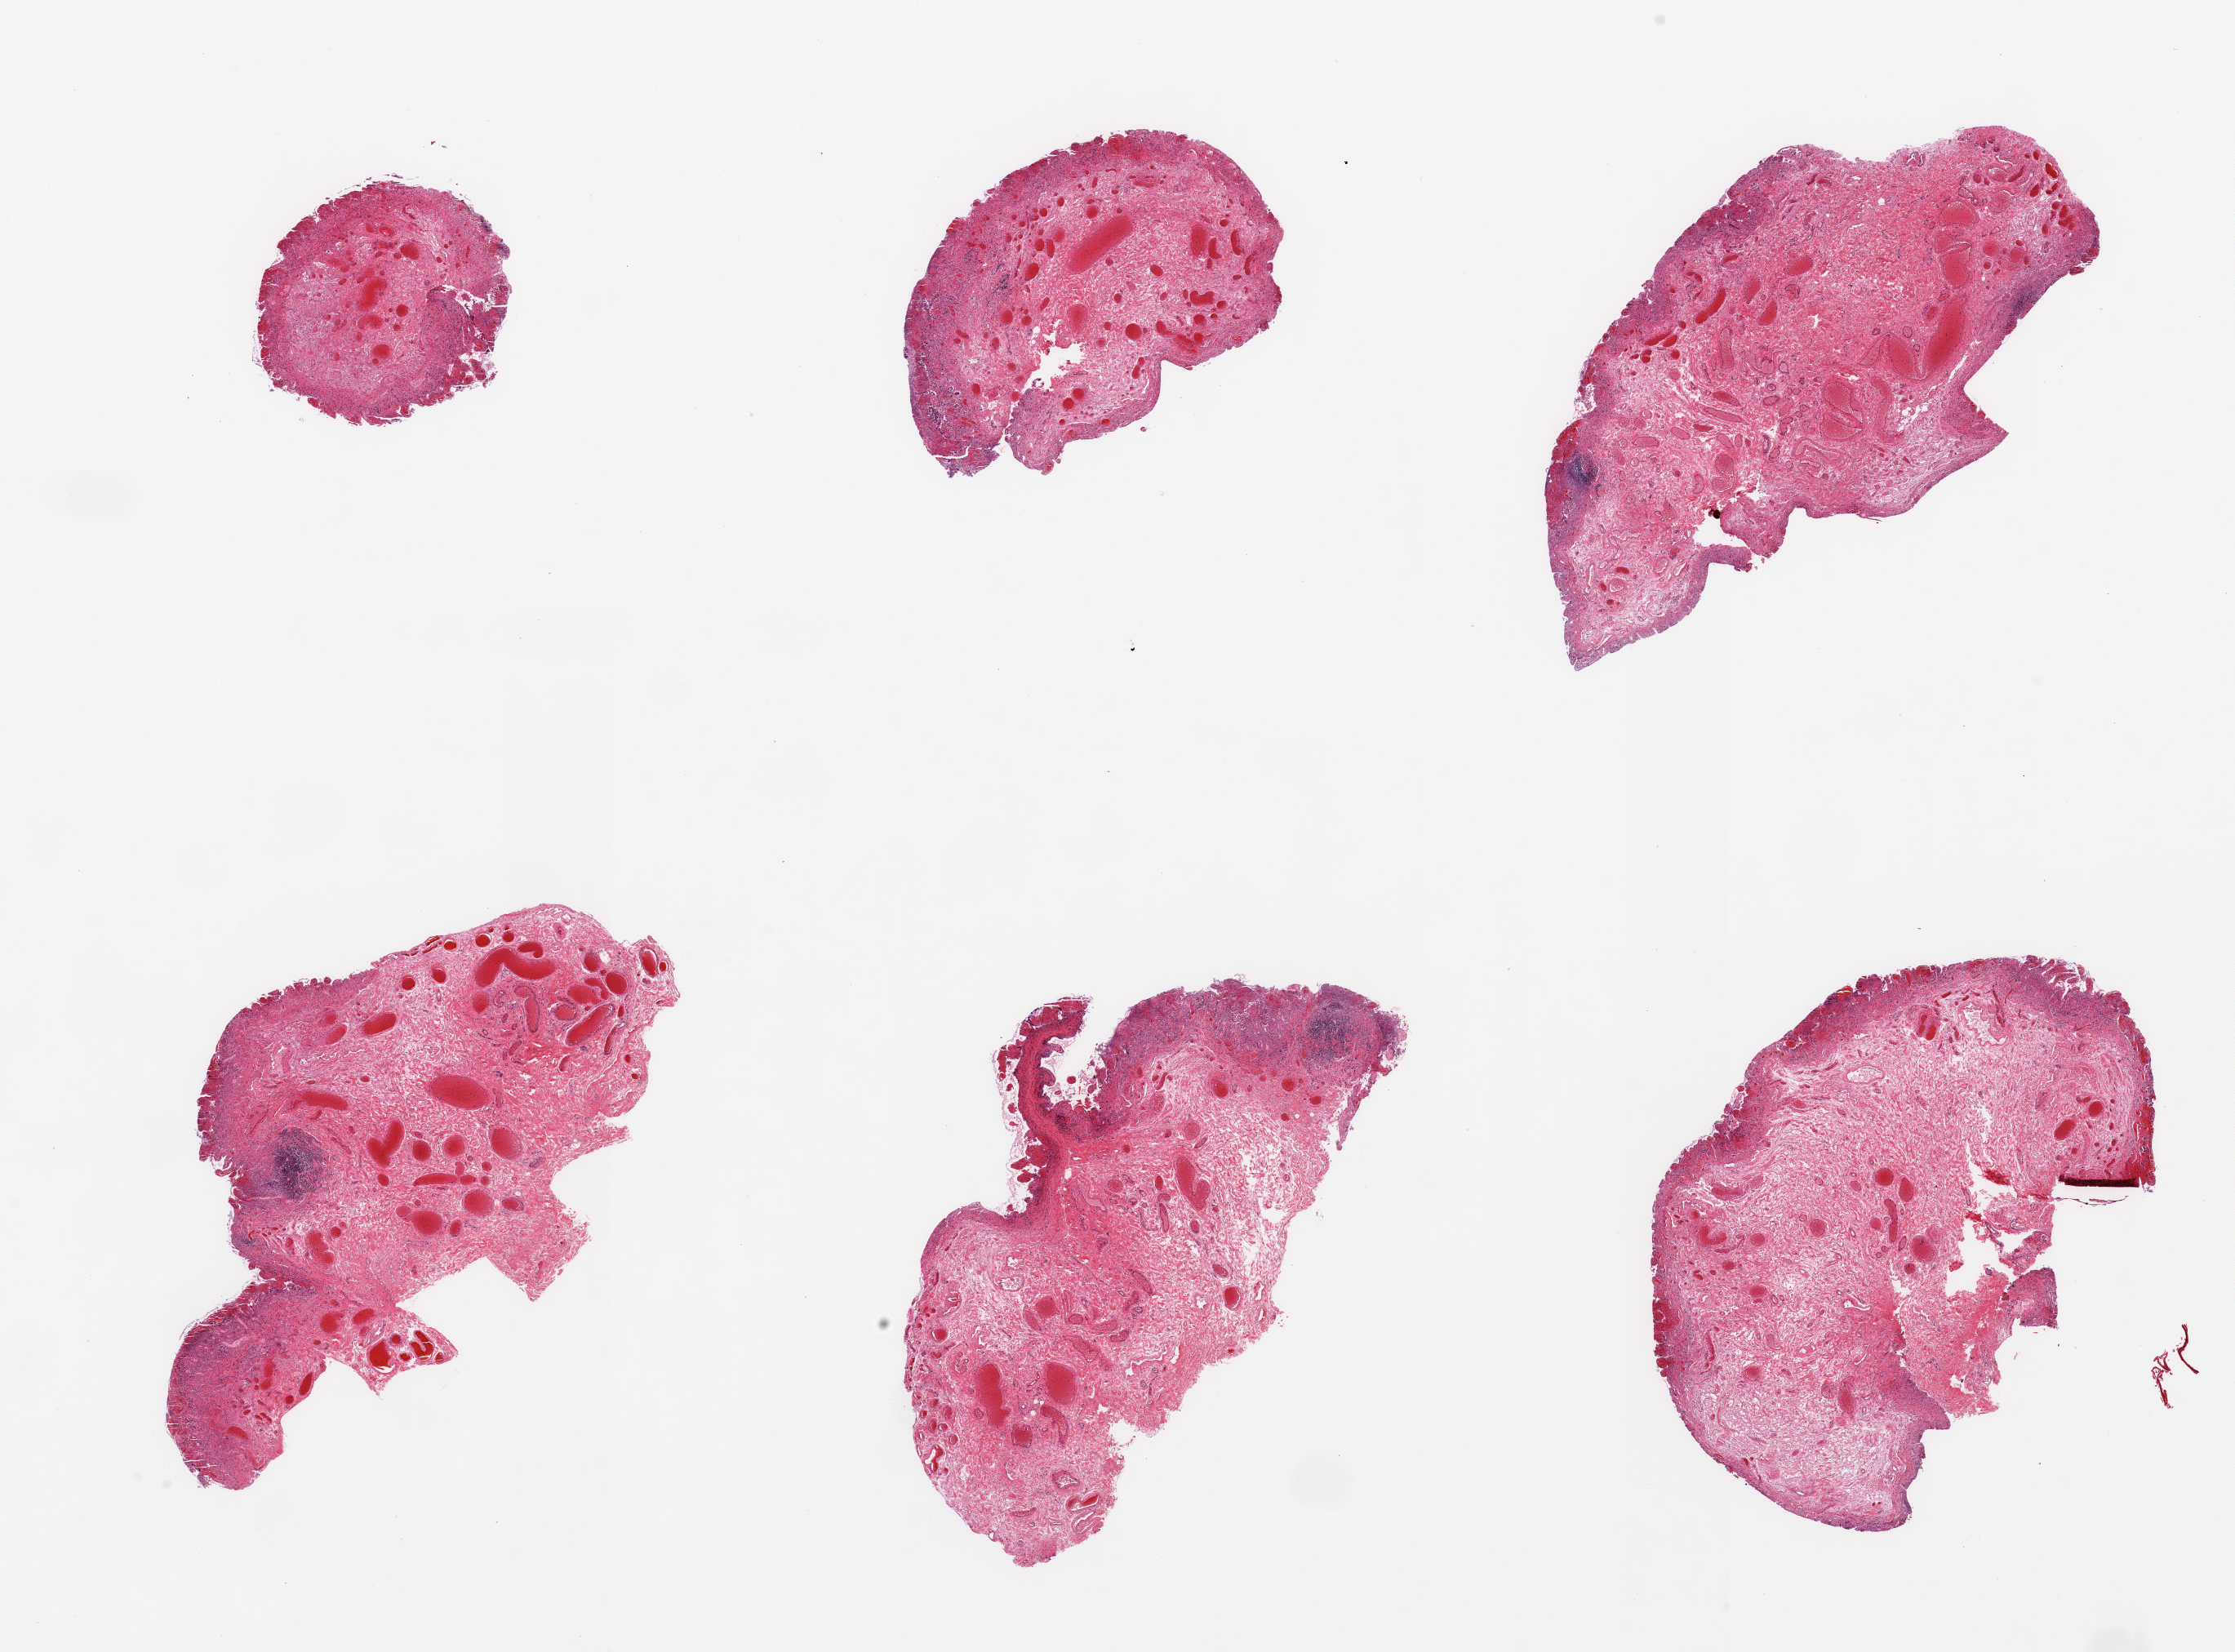
Whole-slide image, haematoxylin and eosin stain, brightfield, shown as a low-resolution overview of the whole scanned area (about 21.7 x 16.0 mm, acquisition: 20x scan); PAXgene-fixed paraffin-embedded (PFPE) section; target tissue: ileum; donor tissue sample. Donor sex: male.
Review note (as recorded): 6 pieces, mucosa completely sloughed, <5% target lymphoid elements.